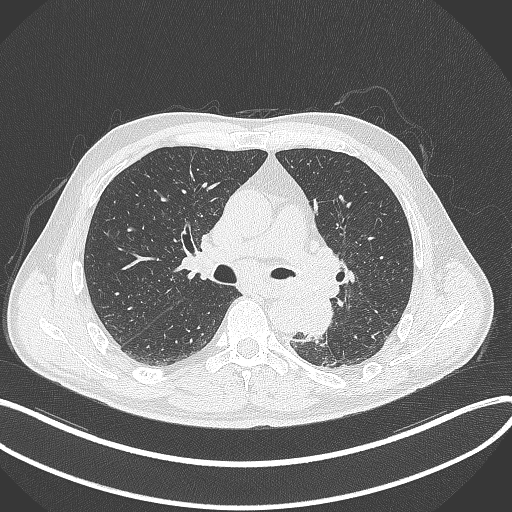
Chest CT, one axial slice; slice 205 of 329 in the series (ordered by position); reconstruction kernel B70f; 120 kVp; lung window (W 1500 / L -600 HU); 512 × 512 image matrix. Patient: male, 59 years. Case-level facts recorded for this patient, not image findings: clinical TNM (as recorded): T2a N2 M0.
Outlined on this slice (bounding box drawn by a radiologist):
- lung tumour (recorded histology: squamous cell carcinoma): bounding box [x1, y1, x2, y2] px = [293, 290, 337, 339]